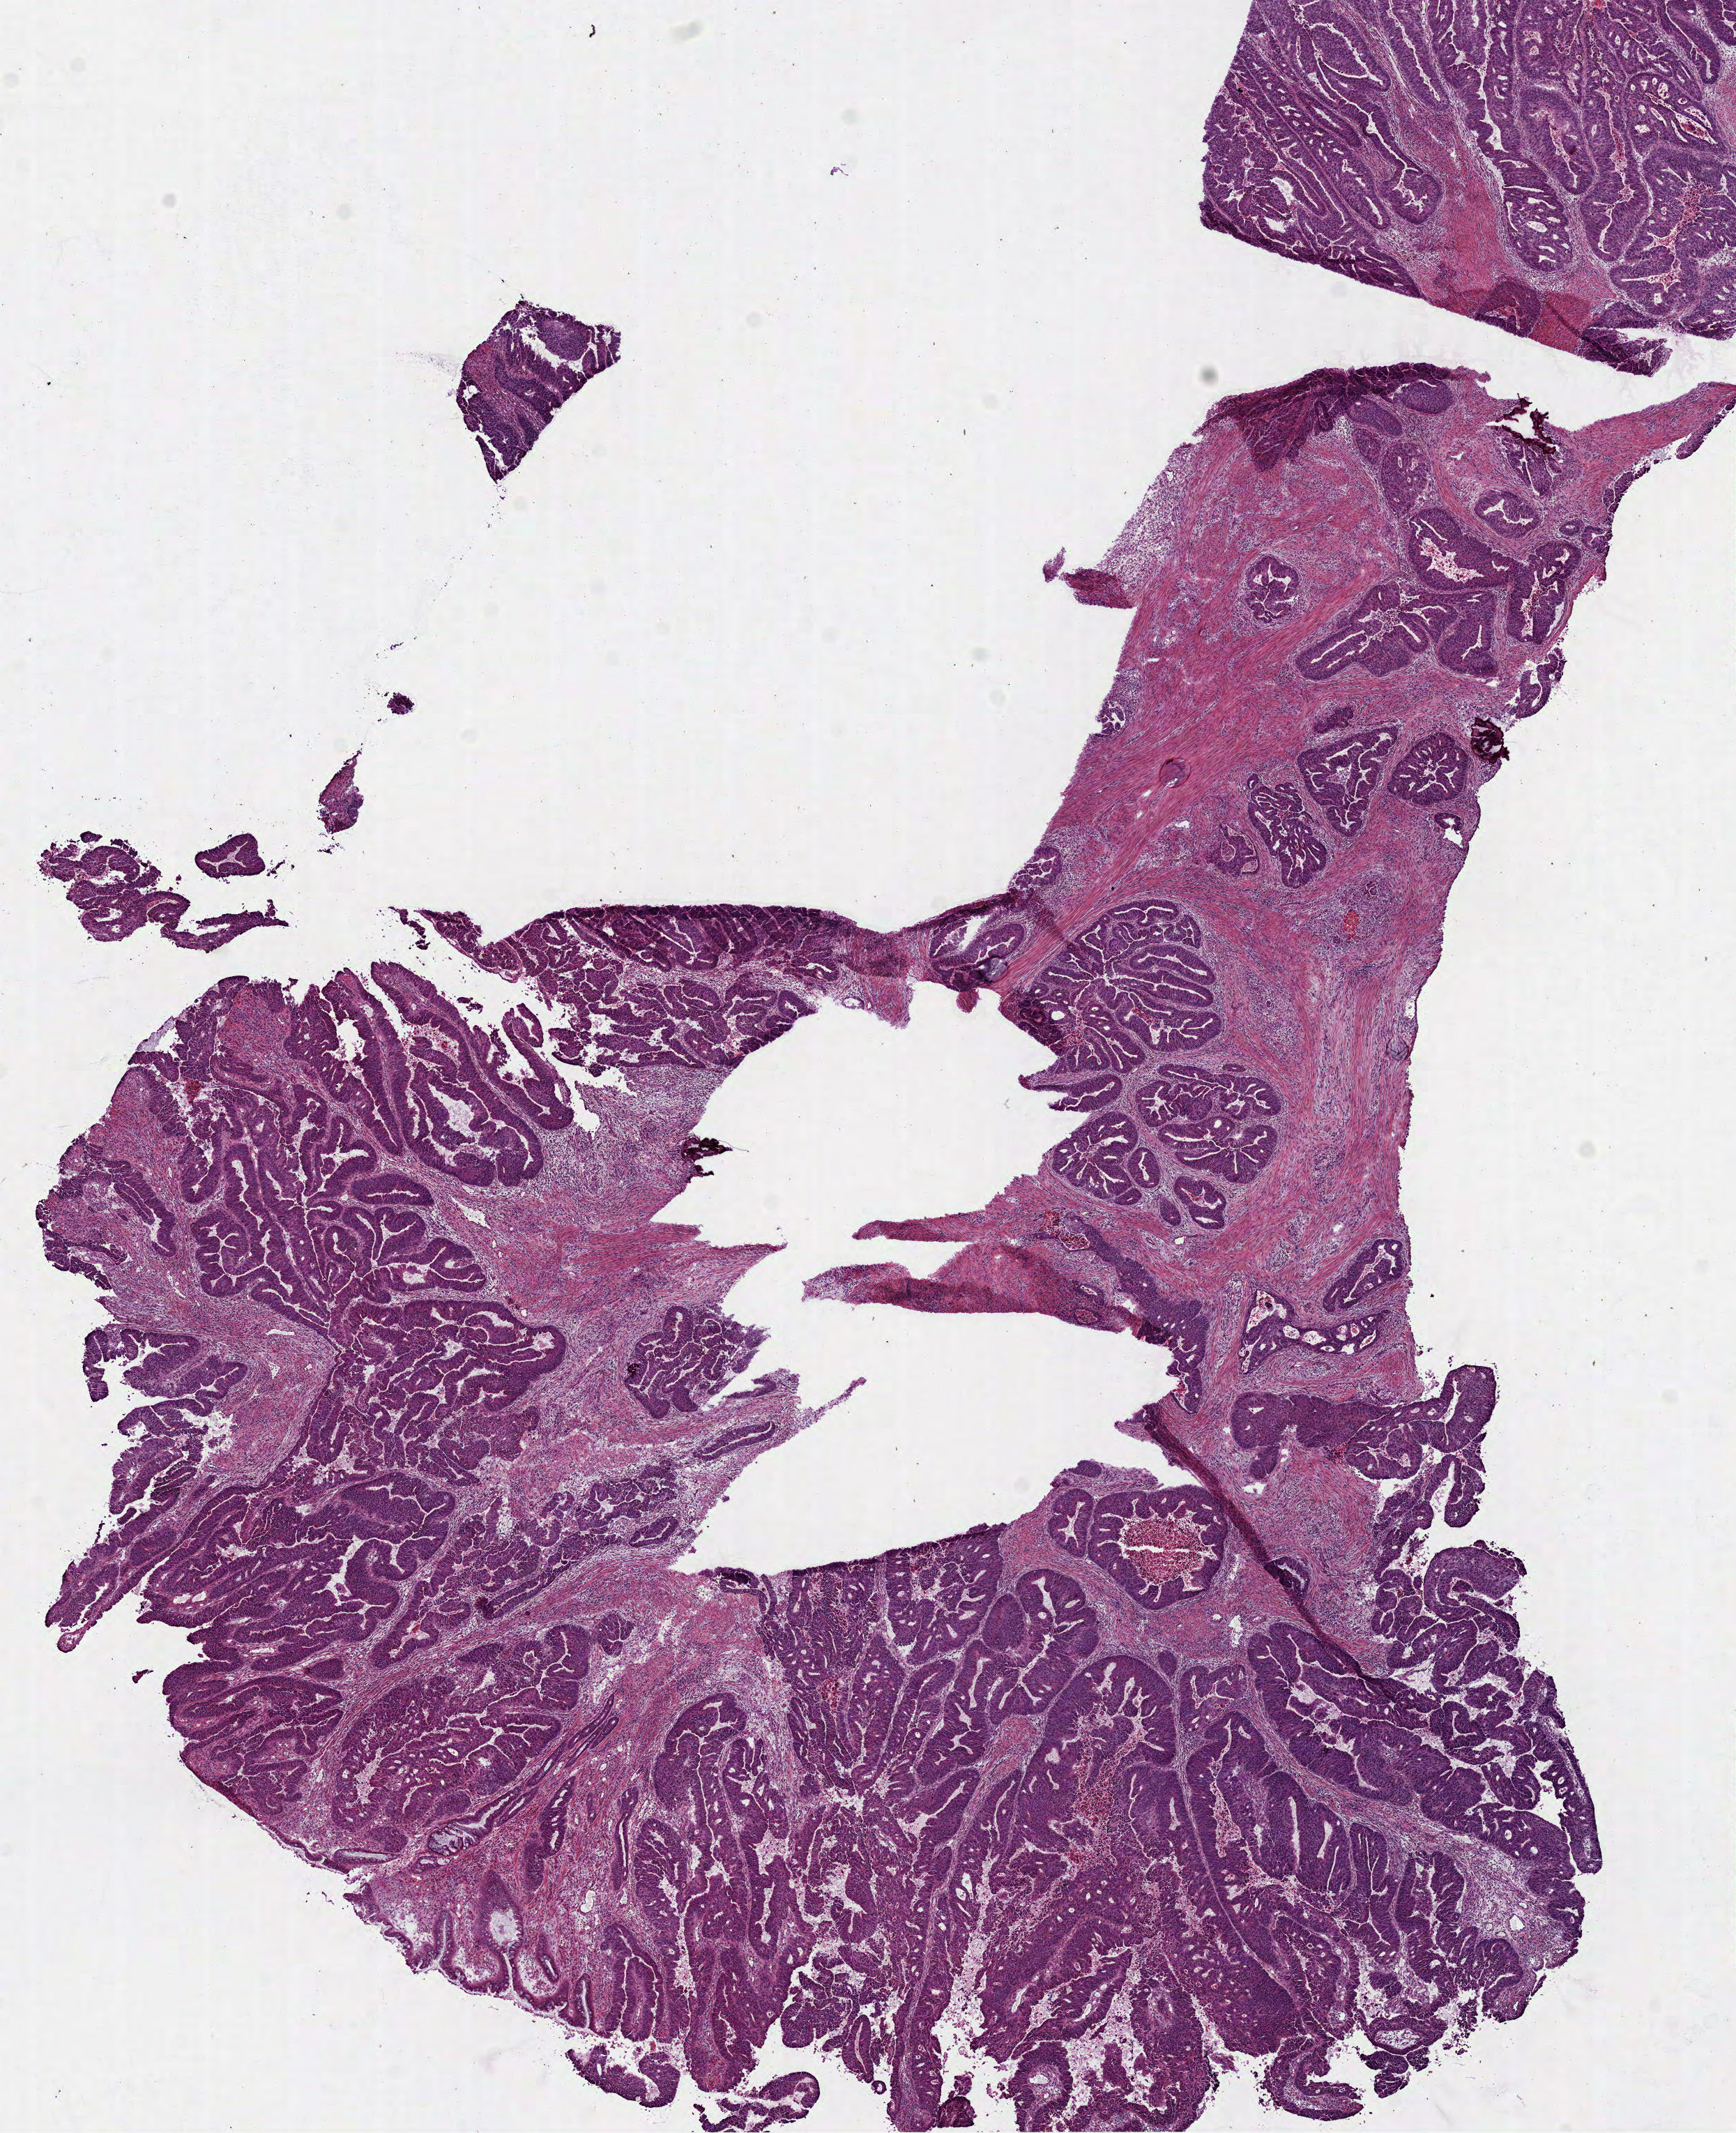
Digitized Hematoxylin and eosin (H&E) stained tissue section (whole slide), shown as a low-resolution overview of the whole scanned area (about 10.0 x 12.3 mm, slide scanned at 40x); frozen section from the bottom of the tissue portion; colon, primary tumour sample. Male patient; age at initial diagnosis 82 years.
Pathologic diagnosis: Adenocarcinoma, NOS (sigmoid colon).